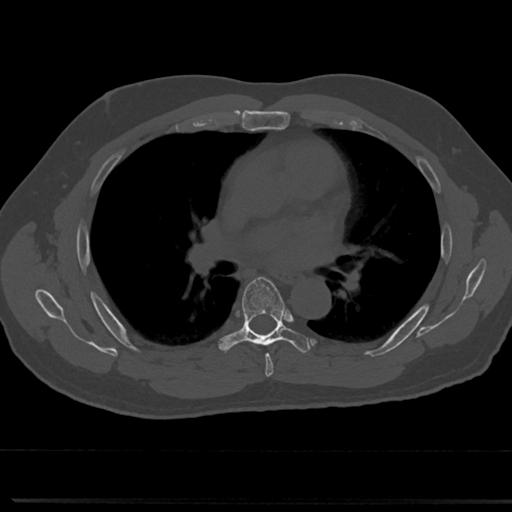
CT including the spine, one axial slice. Slice 460 of 817 in the series (ordered by position). 120 kVp. Bone window (W 1800 / L 400 HU). 0.5 mm slice thickness. 512 × 512 image matrix. Male patient, age 61 years. Case-level facts recorded for this patient, not image findings: primary cancer: prostate.
Structures marked on this image (semi-automatically segmented with operator editing):
- T5 vertebra: bounding box [x1, y1, x2, y2] px = [256, 340, 273, 368]
- T6 vertebra: [217, 275, 309, 356]